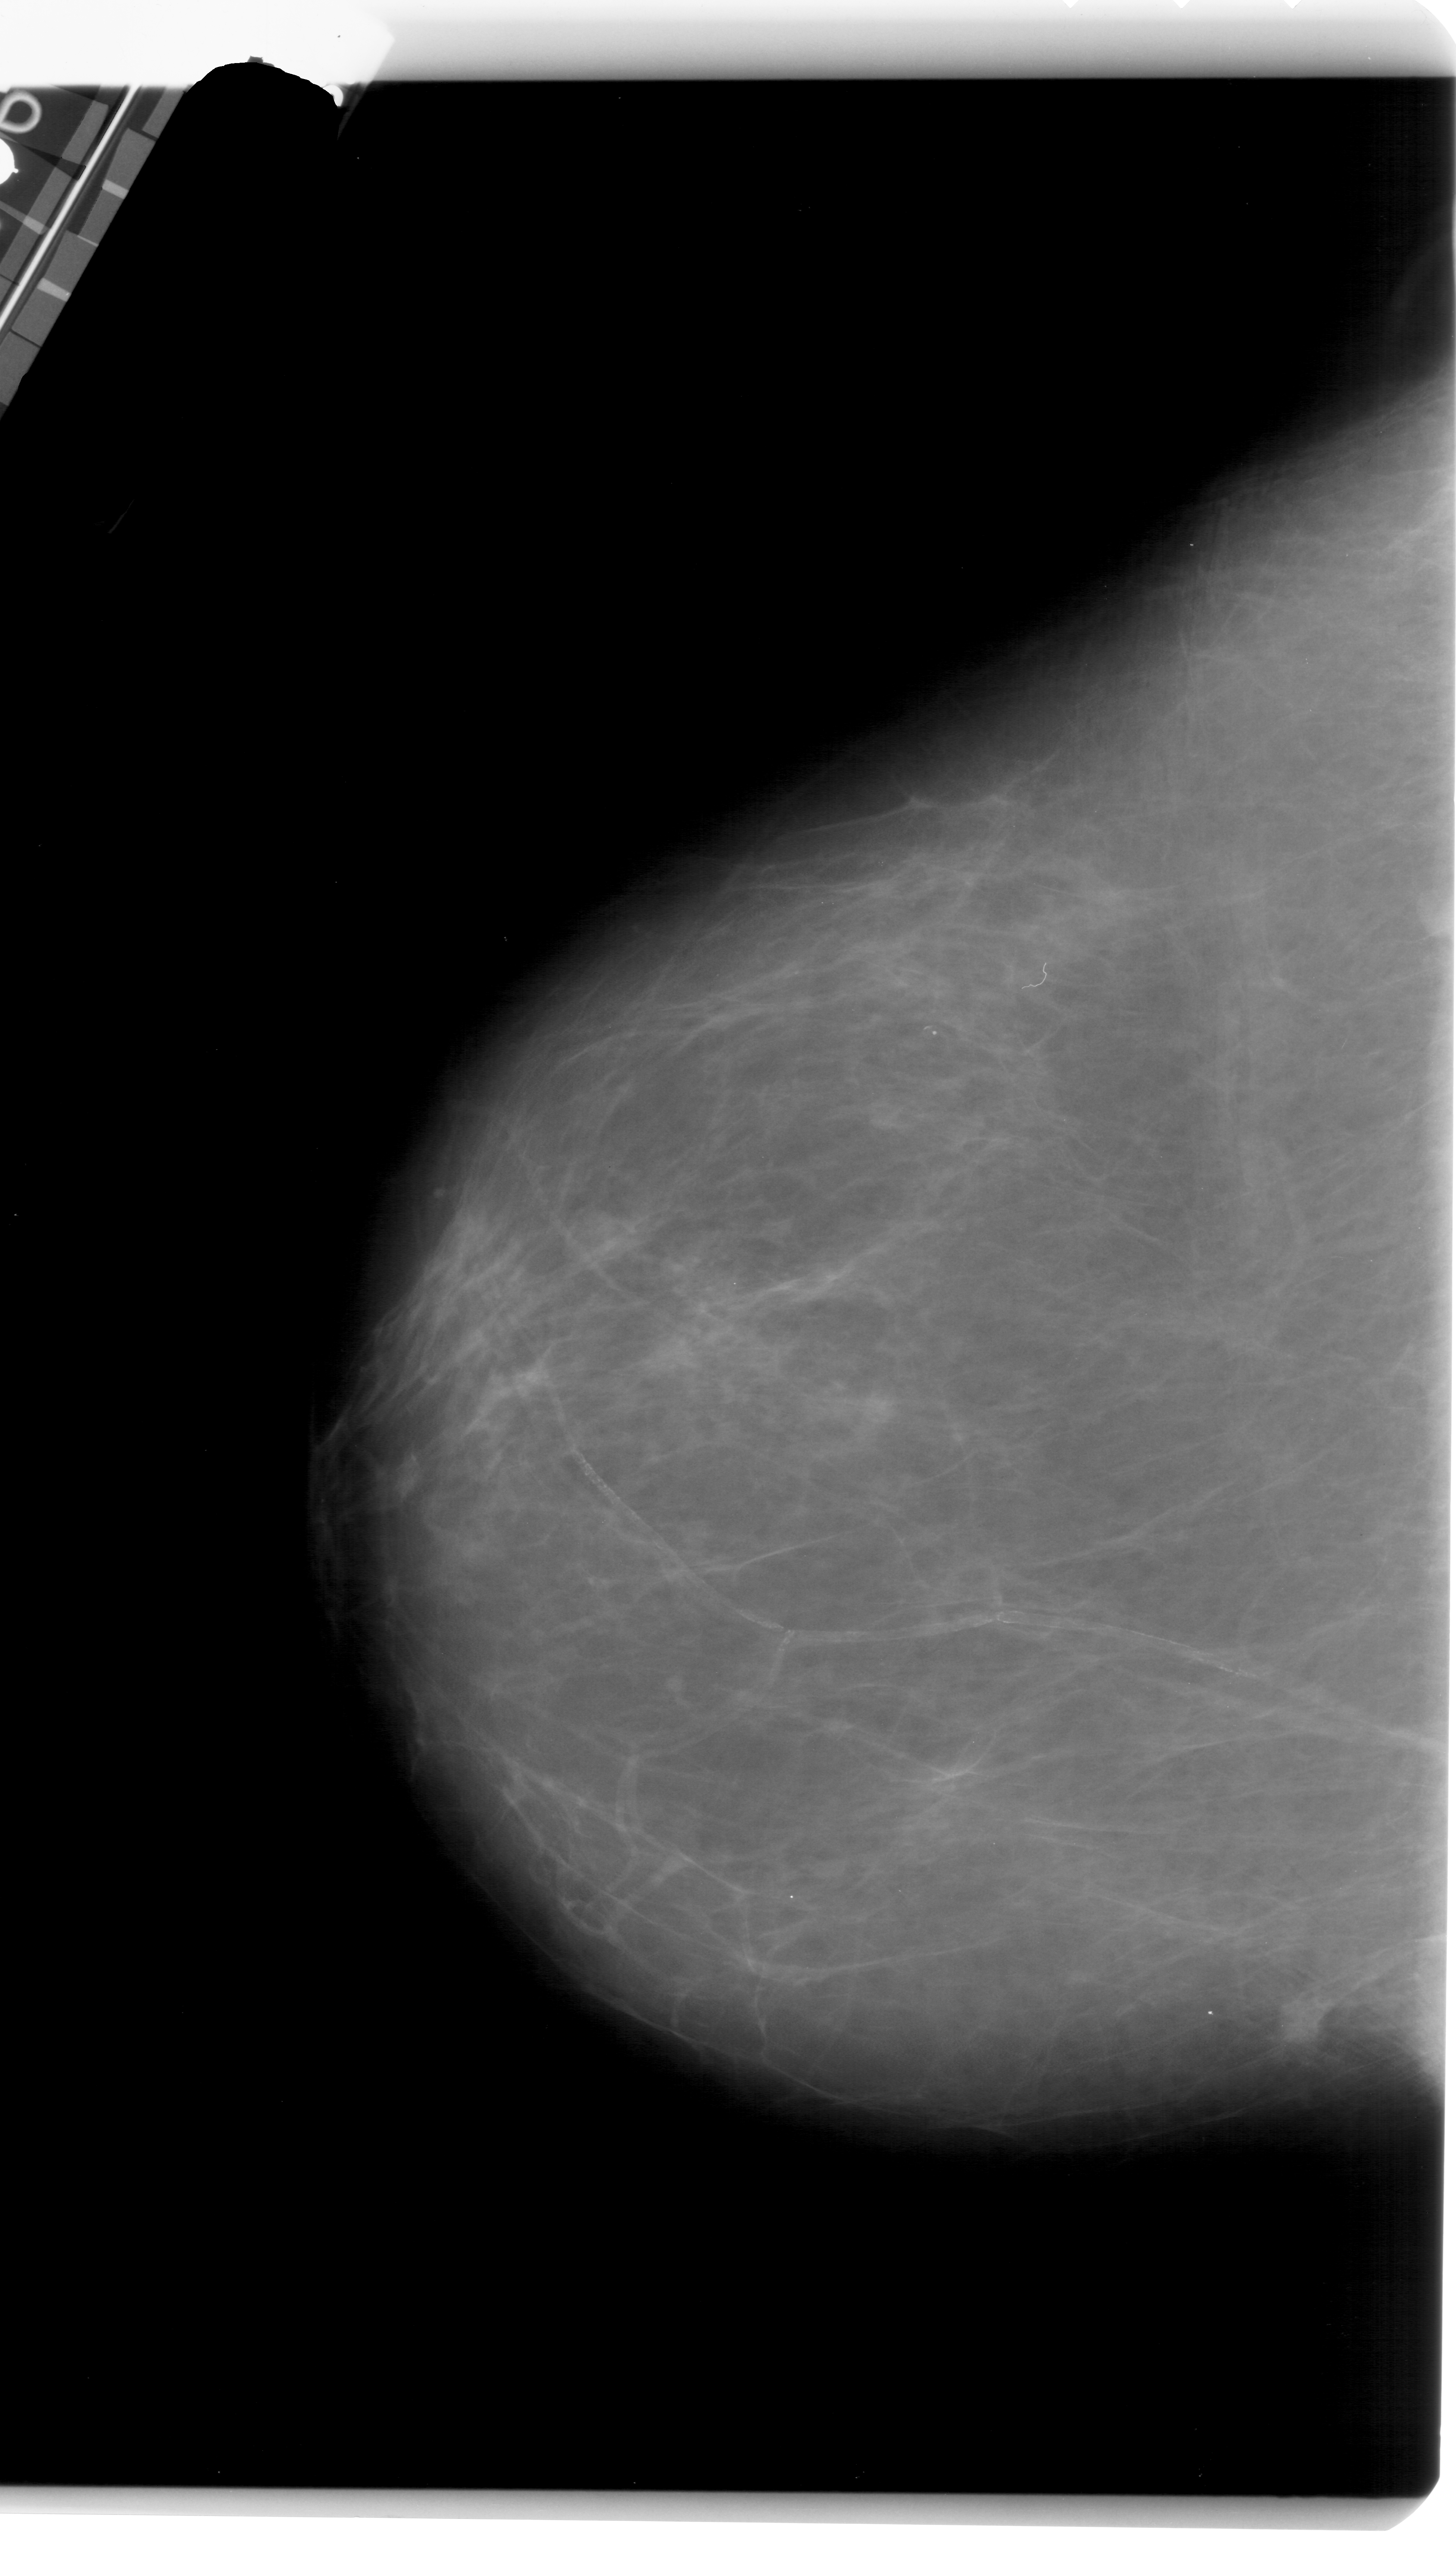
Scanned film-screen mammogram. Left breast. Craniocaudal (CC) view. BI-RADS breast density category 2 (scale 1–4). 1456 × 2559 image matrix.
Expert-marked regions of interest on this film, with their recorded descriptors:
- mass, shape irregular, margins ill defined; BI-RADS assessment category 4; pathology result (as recorded, not read from the image): malignant: bounding box <1277,1990,1334,2048> (left, top, right, bottom; pixels)